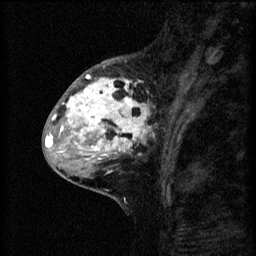
Breast MRI (dynamic contrast-enhanced), one sagittal slice; slice 24 of 60 in the series (ordered by position); 3 images stored at this slice position (order not interpretable as contrast timing); 1.5 T; TE 4.2 ms, TR 8.2 ms; 256 × 256 image matrix. Female patient, age 41 years.
Structures marked on this image (semi-automatic segmentation, software-assisted and operator-edited):
- analysis volume of interest (the breast-tissue region the enhancement analysis was run in; not a lesion): bounding box [x1, y1, x2, y2] px = [53, 62, 155, 175]
- tumour enhancement mask (voxels above the 70 % enhancement threshold inside the analysis volume of interest): [53, 74, 155, 173]